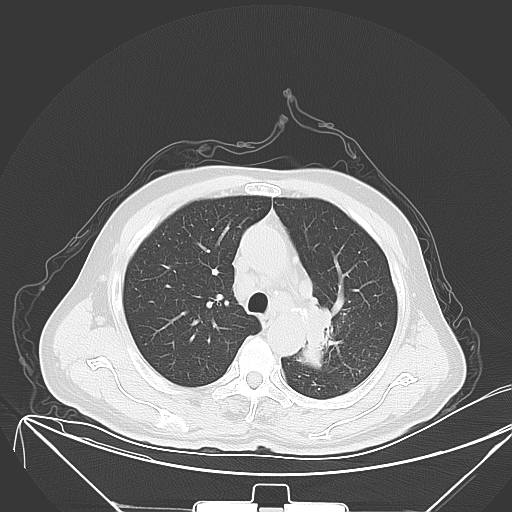
Chest CT, one axial slice; position 42 of 64 along the scan axis; 120 kVp; lung window (W 1500 / L -600 HU); 512 × 512 image matrix, field of view 431 × 431 mm. Male patient, age 58 years. From the clinical record (not read from this slice): clinical TNM (as recorded): T2b N3 M1b.
Structures marked on this image (bounding box drawn by a radiologist):
- lung tumour (recorded histology: adenocarcinoma): bounding box (x1, y1, x2, y2) in pixels: (298, 298, 335, 374)